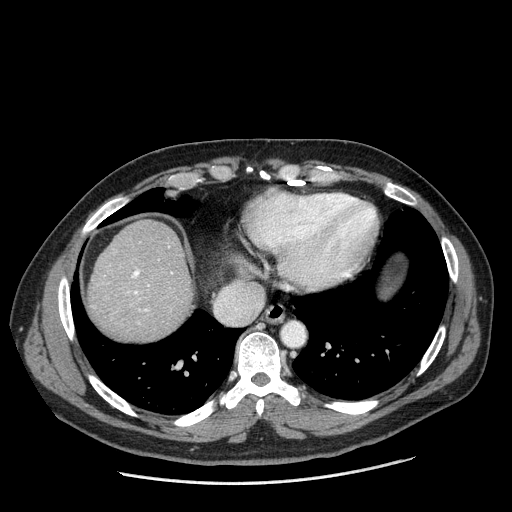
Contrast-enhanced abdominal CT (liver protocol), one axial slice. Position 169 of 198 along the scan axis. One of 2 acquisitions stored at this slice position. Soft-tissue window (W 400 / L 40 HU). 2.5 mm slice thickness. 512 × 512 image matrix, field of view 400 × 400 mm. From the clinical record (not read from this slice): diagnosis: hepatocellular carcinoma (patient treated with transarterial chemoembolisation; whether this scan precedes or follows treatment is not stated here); TNM stage (as recorded): Stage-II; Child-Pugh class: A; tumour nodularity: multinodular; tumour size: 2.6 cm.
Structures marked on this image (semi-automatically segmented with operator editing):
- abdominal aorta: box from (x=282, y=323) to (x=304, y=345) px
- liver parenchyma outside the tumour (the mass and vessels are separate outlines, so this box may not span the whole liver): (x=88, y=220)–(x=192, y=340)
- liver vessels: (x=131, y=269)–(x=173, y=312)